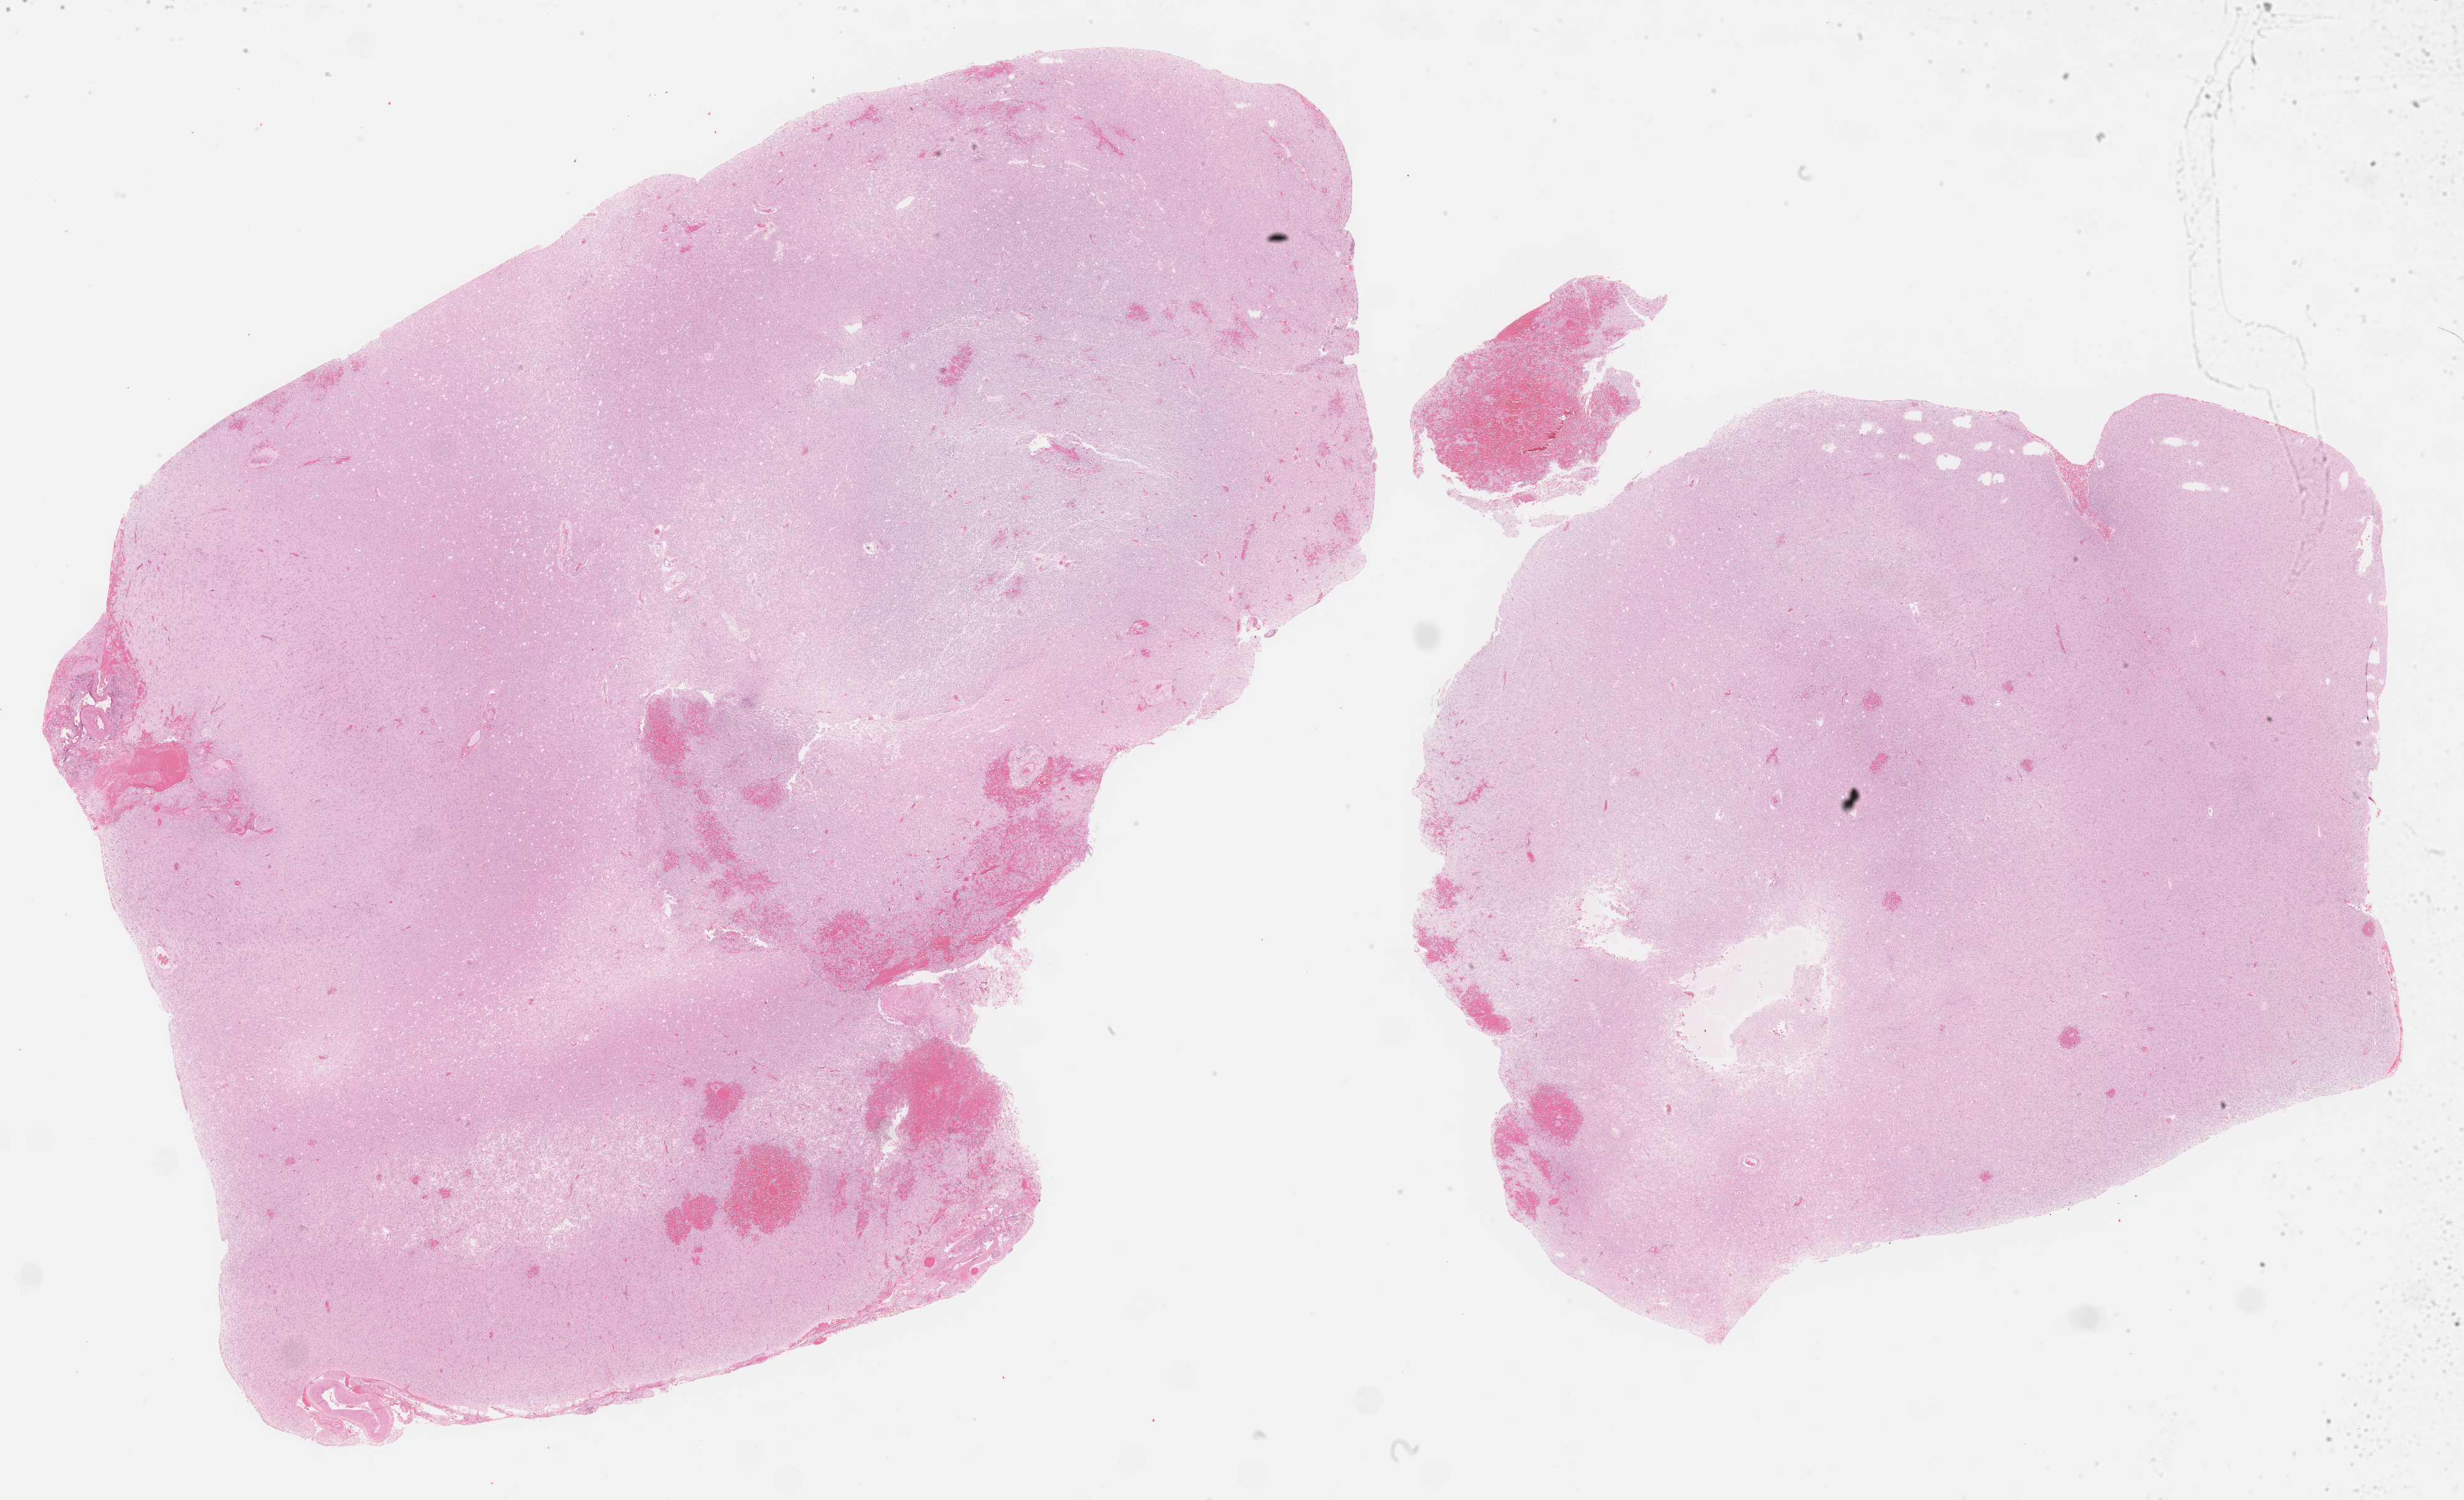
Whole-slide histology image, Hematoxylin and eosin (H&E) stained, low-resolution overview of the scanned area, about 31.9 x 19.4 mm (acquisition: 40x scan). FFPE section. Sample: primary tumour, brain. Male patient; age at initial diagnosis 52 years. Histologic grade: G3 (poorly differentiated).
- pathologic diagnosis: Oligodendroglioma, anaplastic (cerebrum)
- laterality: left